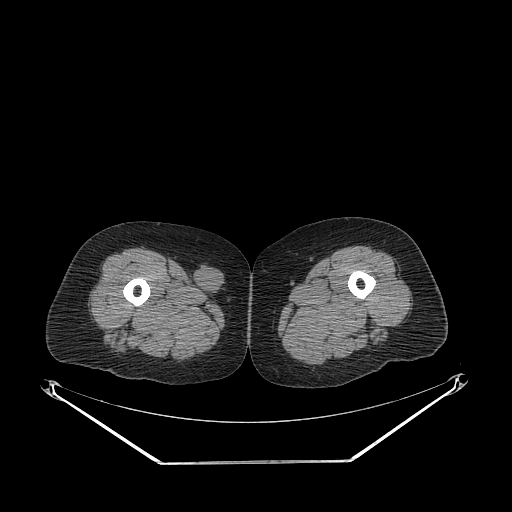
CT of an extremity soft-tissue mass (from a PET/CT study), one axial slice. Position 242 of 311 along the scan axis. Reconstruction kernel STANDARD. 140 kVp. Soft-tissue window (W 400 / L 40 HU). 3.75 mm slice thickness. 512 × 512 image matrix, field of view 500 × 500 mm. Female patient. Case-level facts recorded for this patient, not image findings: histological type: leiomyosarcoma; grade: intermediate; site of the primary tumour: parascapusular.
Outlined on this slice (expert contour drawn on MRI and transferred to this co-registered scan by the dataset authors):
- gross tumour volume including surrounding oedema: bounding box [x1, y1, x2, y2] px = [192, 262, 225, 300]
- gross tumour volume (mass): [196, 262, 225, 291]